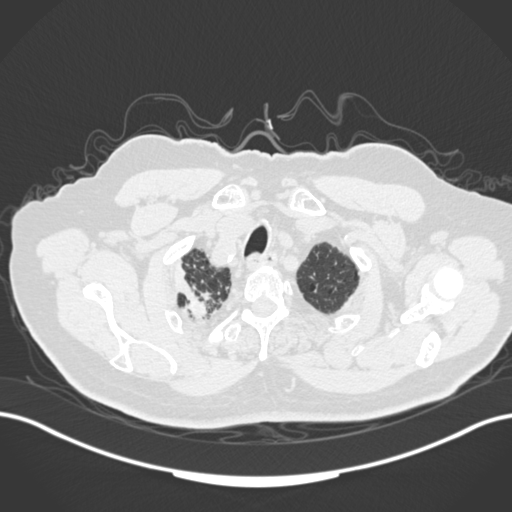
Chest CT, one axial slice; slice 157 of 205 in the series (ordered by position); reconstruction kernel B30f; lung window (W 1500 / L -600 HU); 1 mm slice thickness; 512 × 512 image matrix, field of view 400 × 400 mm. Patient: male, 72 years. From the clinical record (not read from this slice): clinical TNM (as recorded): T1a N0 M0.
Annotated regions visible in this slice (bounding box drawn by a radiologist):
- lung tumour (recorded histology: squamous cell carcinoma): bounding box (x1, y1, x2, y2) in pixels: (169, 262, 211, 318)